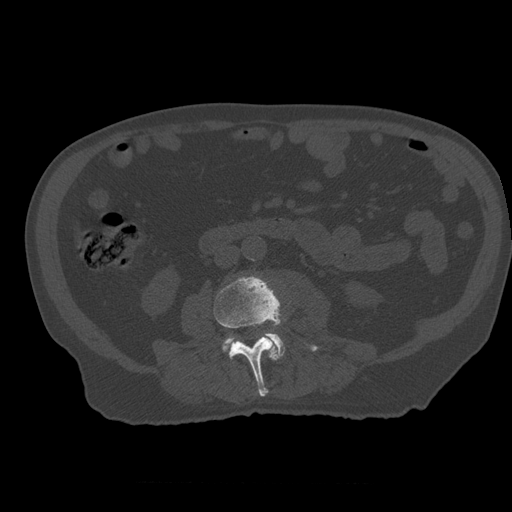
CT including the spine, one axial slice. Position 184 of 399 along the scan axis. Bone window (W 1800 / L 400 HU). 1.25 mm slice thickness. 512 × 512 image matrix, field of view 407 × 407 mm. Patient age 73 years. From the clinical record (not read from this slice): primary cancer: prostate; vertebrae with lytic lesions (as recorded): L2.
Annotated regions visible in this slice (semi-automatically segmented with operator editing):
- L3 vertebra: box from (x=214, y=276) to (x=319, y=397) px
- L4 vertebra: (x=223, y=334)–(x=285, y=356)